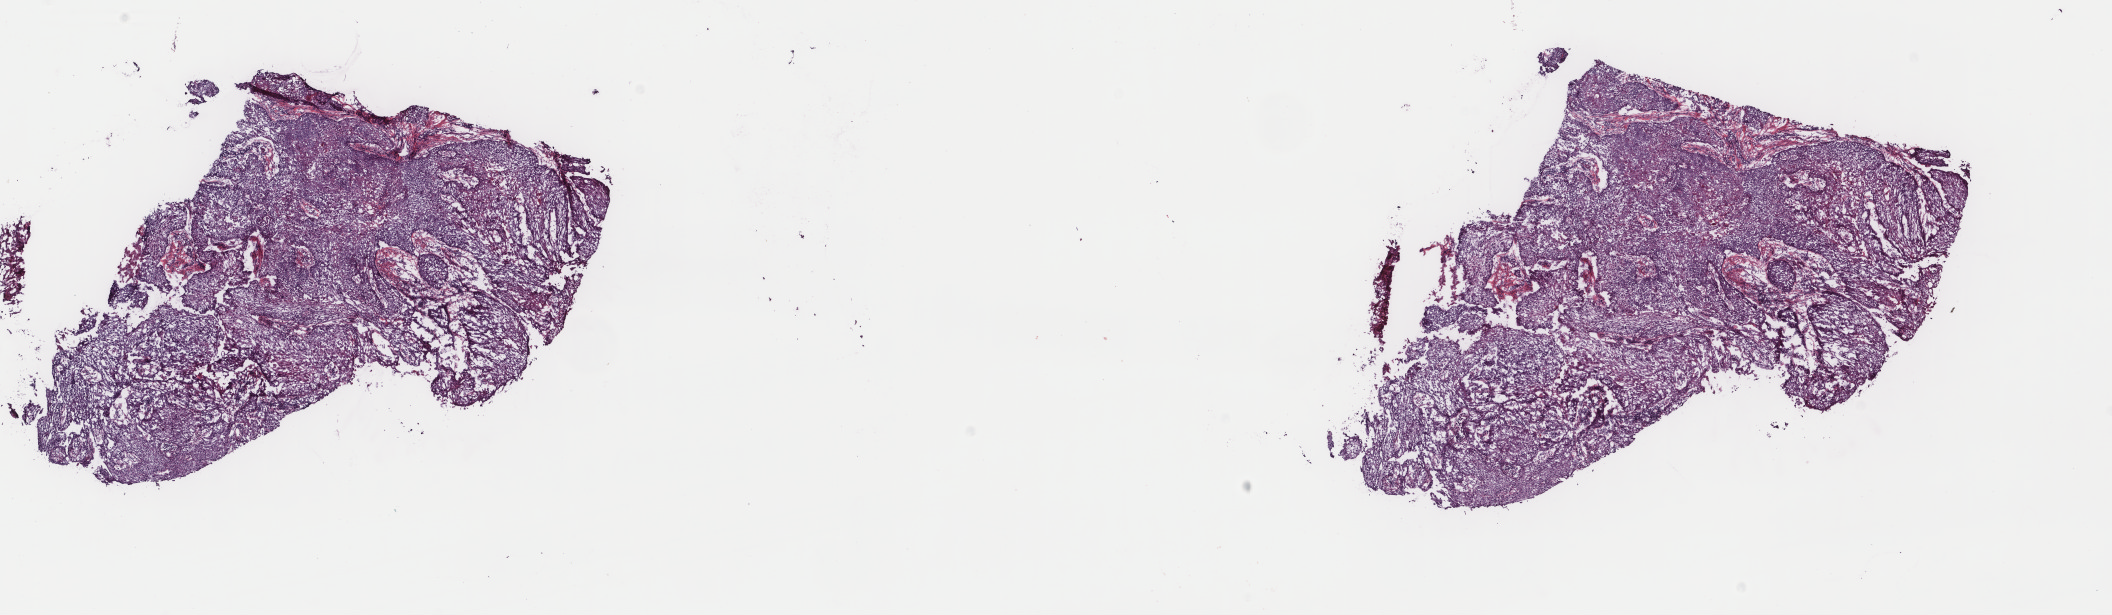
Digitized H&E tissue section (whole slide) — low-resolution overview of the scanned area, about 16.8 x 4.9 mm (from a 40x scan), frozen section, sample: primary tumour, esophagus. Patient: male, age at initial diagnosis 59 years. Histologic grade: G2 (moderately differentiated). Pathologist review of this section (percent, as recorded): tumour cells 75%, tumour nuclei 90%, normal cells 0%, stromal cells 20%, necrosis 5%. Infiltration values recorded for this section: lymphocyte infiltration 4%, monocyte infiltration 0%, neutrophil infiltration 1%.
Diagnosis: Squamous cell carcinoma, NOS (lower third of esophagus). TNM: T3 N0 M0. AJCC pathologic stage: IIA (6th edition).